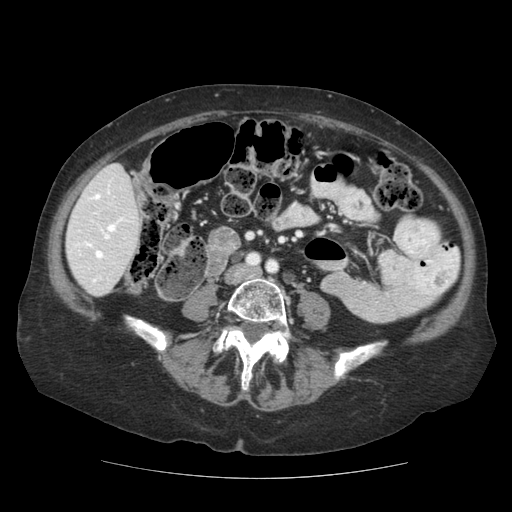
Contrast-enhanced abdominal CT (liver protocol), one axial slice. Position 31 of 111 along the scan axis. Reconstruction kernel STANDARD. Soft-tissue window (W 400 / L 40 HU). 512 × 512 image matrix, field of view 360 × 360 mm. Case-level facts recorded for this patient, not image findings: diagnosis: hepatocellular carcinoma (patient treated with transarterial chemoembolisation; whether this scan precedes or follows treatment is not stated here); TNM stage (as recorded): Stage-I; Child-Pugh class: A; tumour differentiation: moderately-poorly differentiated; tumour nodularity: uninodular.
Annotated regions visible in this slice (semi-automatic segmentation, software-assisted and operator-edited):
- liver parenchyma outside the tumour (the mass and vessels are separate outlines, so this box may not span the whole liver): box from (x=66, y=164) to (x=140, y=296) px
- liver vessels: (x=69, y=186)–(x=124, y=282)